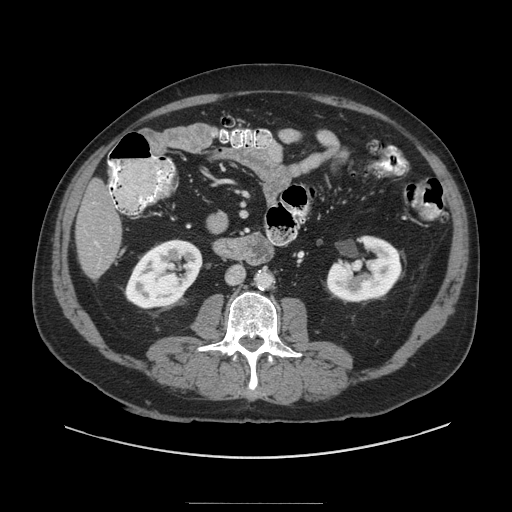
Contrast-enhanced abdominal CT (liver protocol), one axial slice. Position 23 of 91 along the scan axis. 140 kVp. Soft-tissue window (W 400 / L 40 HU). 2.5 mm slice thickness. 512 × 512 image matrix, field of view 440 × 440 mm. Case-level facts recorded for this patient, not image findings: diagnosis: hepatocellular carcinoma (patient treated with transarterial chemoembolisation; whether this scan precedes or follows treatment is not stated here); TNM stage (as recorded): Stage-I; Child-Pugh class: A; tumour differentiation: well differentiated; tumour nodularity: uninodular.
Structures marked on this image (semi-automatic segmentation, software-assisted and operator-edited):
- liver parenchyma outside the tumour (the mass and vessels are separate outlines, so this box may not span the whole liver): bounding box (x1, y1, x2, y2) in pixels: (76, 178, 122, 278)
- liver vessels: (94, 241, 99, 246)